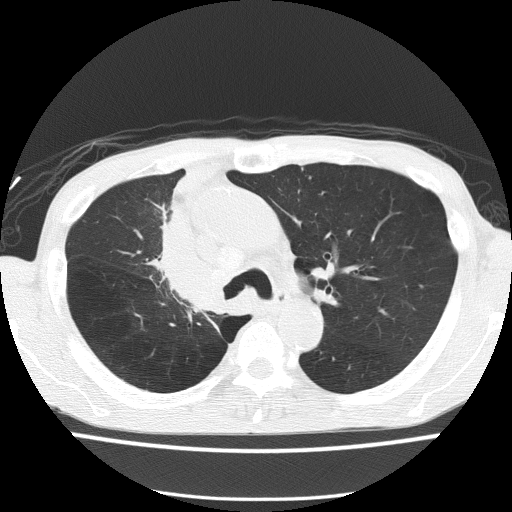
Low-dose screening chest CT, axial slice; baseline annual screen; lung window (W 1500 / L -600 HU); 2 mm slice thickness; slice 50 of 150 in the series. Male, age 59 years at enrolment.
- Lesion marked by an expert reader, bounding box [x1, y1, x2, y2] px = [138, 231, 234, 322].
- The screening reader recorded 5 non-calcified nodules or masses ≥4 mm on this exam (left upper lobe, left upper lobe, left upper lobe, right middle lobe, right lower lobe); which of them this box marks is not recorded.
- Official screen result: positive, change unspecified: nodule(s) >= 4 mm or enlarging nodule(s), mass(es), or other non-specific abnormalities suspicious for lung cancer.
- Participant outcome: lung cancer diagnosed 72 days after this screen — squamous cell carcinoma, NOS, right upper lobe, moderately differentiated (G2), stage IV (AJCC 6th edition).